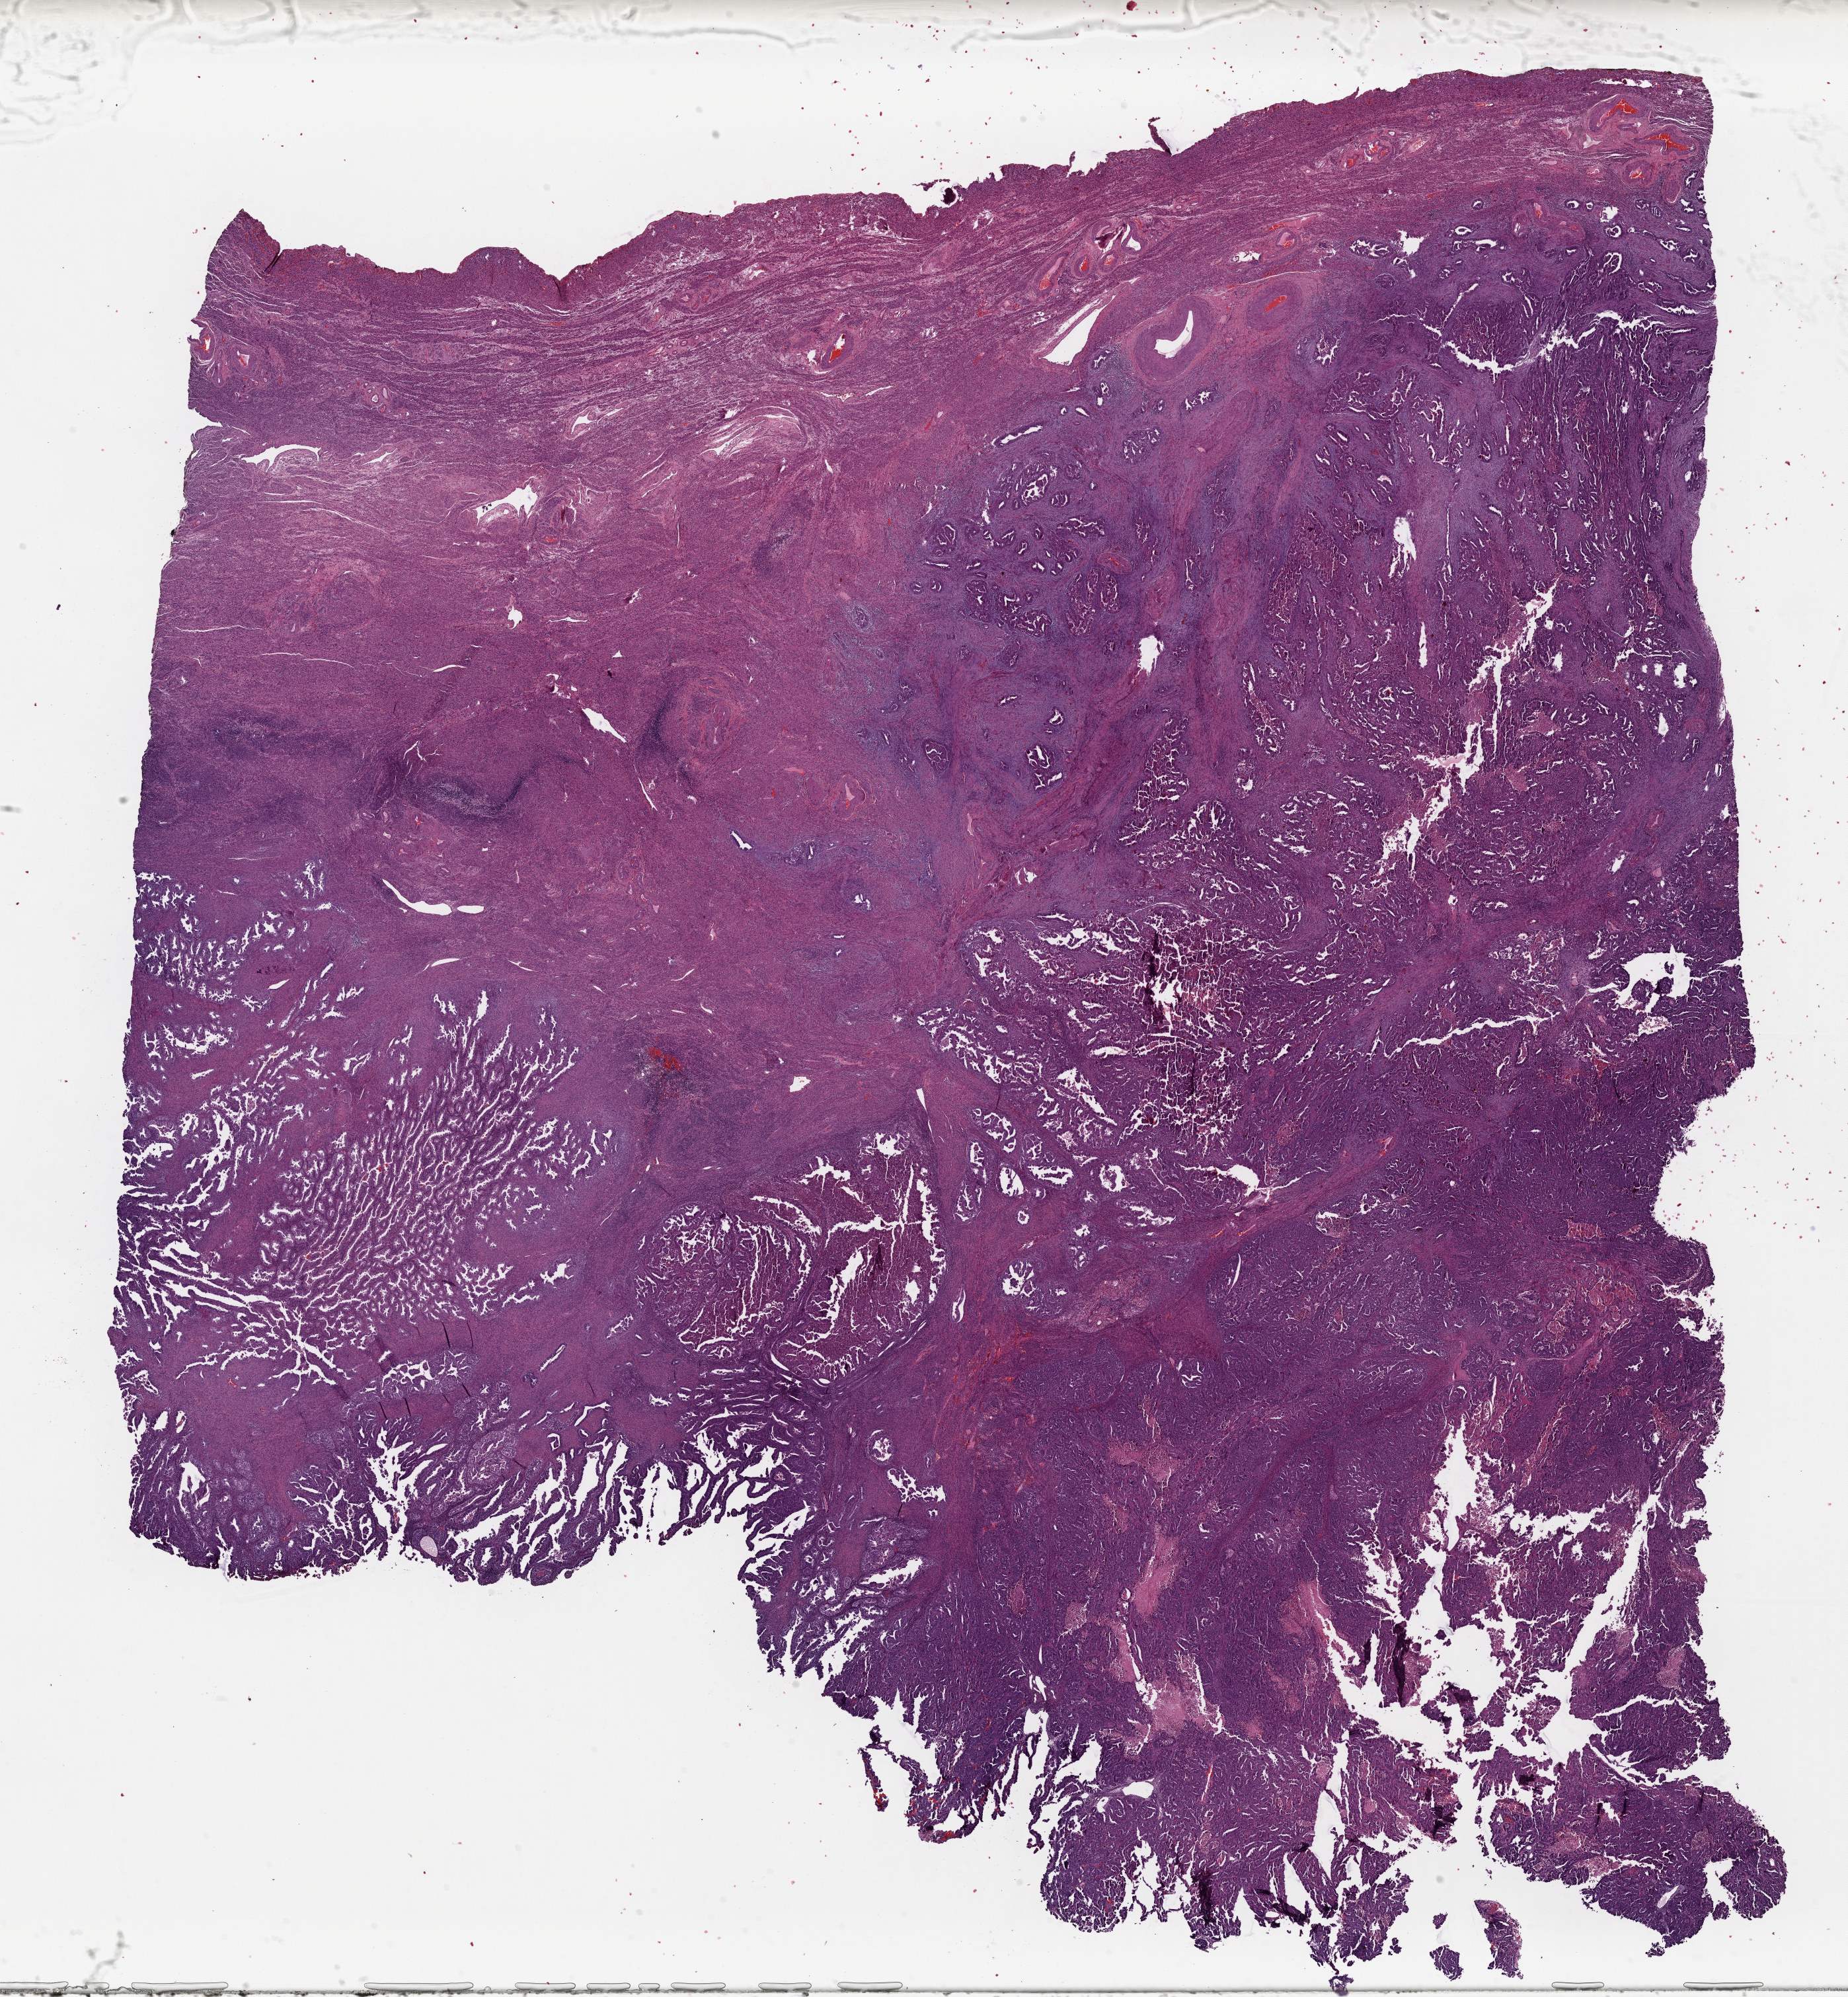
Whole-slide histology image, H&E-stained — a low-resolution overview of the entire scanned area, about 22.0 x 23.7 mm; formalin-fixed paraffin-embedded (FFPE) diagnostic section; primary tumour sample from the uterus. Female, age 60 years at initial diagnosis. Histologic grade: G3 (poorly differentiated).
FIGO stage: IVB. Diagnosis: Serous cystadenocarcinoma, NOS (endometrium).